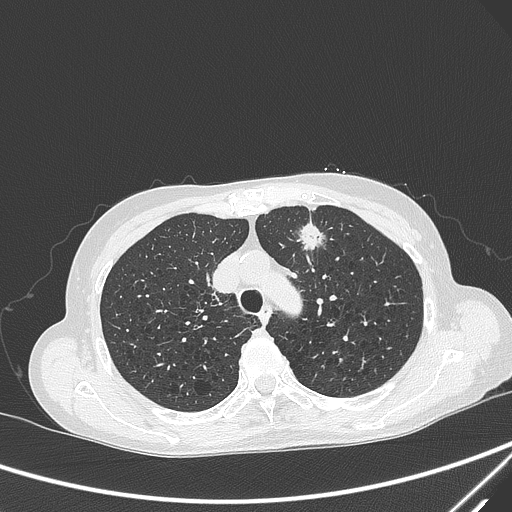
Chest CT, one axial slice. Position 227 of 299 along the scan axis. 120 kVp. Lung window (W 1500 / L -600 HU). 512 × 512 image matrix, field of view 350 × 350 mm. Female patient, age 71 years. Case-level facts recorded for this patient, not image findings: clinical TNM (as recorded): T1c N0 M0.
Outlined on this slice (rectangle marked by the reading radiologist):
- lung tumour (recorded histology: adenocarcinoma): box from (x=295, y=220) to (x=328, y=261) px